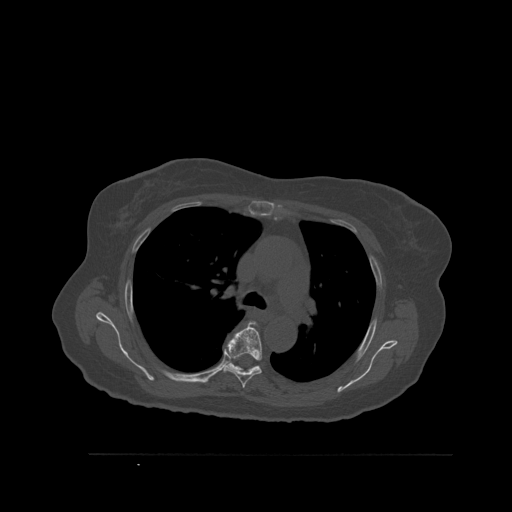
CT including the spine, one axial slice. Slice 392 of 527 in the series (ordered by position). Bone window (W 1800 / L 400 HU). 1.5 mm slice thickness. 512 × 512 image matrix, field of view 470 × 470 mm. Patient: female, 73 years. Case-level facts recorded for this patient, not image findings: primary cancer: breast; vertebrae with lytic lesions (as recorded): L2.
Structures marked on this image (semi-automatic segmentation, software-assisted and operator-edited):
- T5 vertebra: box from (x=222, y=322) to (x=262, y=389) px
- T6 vertebra: (x=226, y=363)–(x=261, y=373)